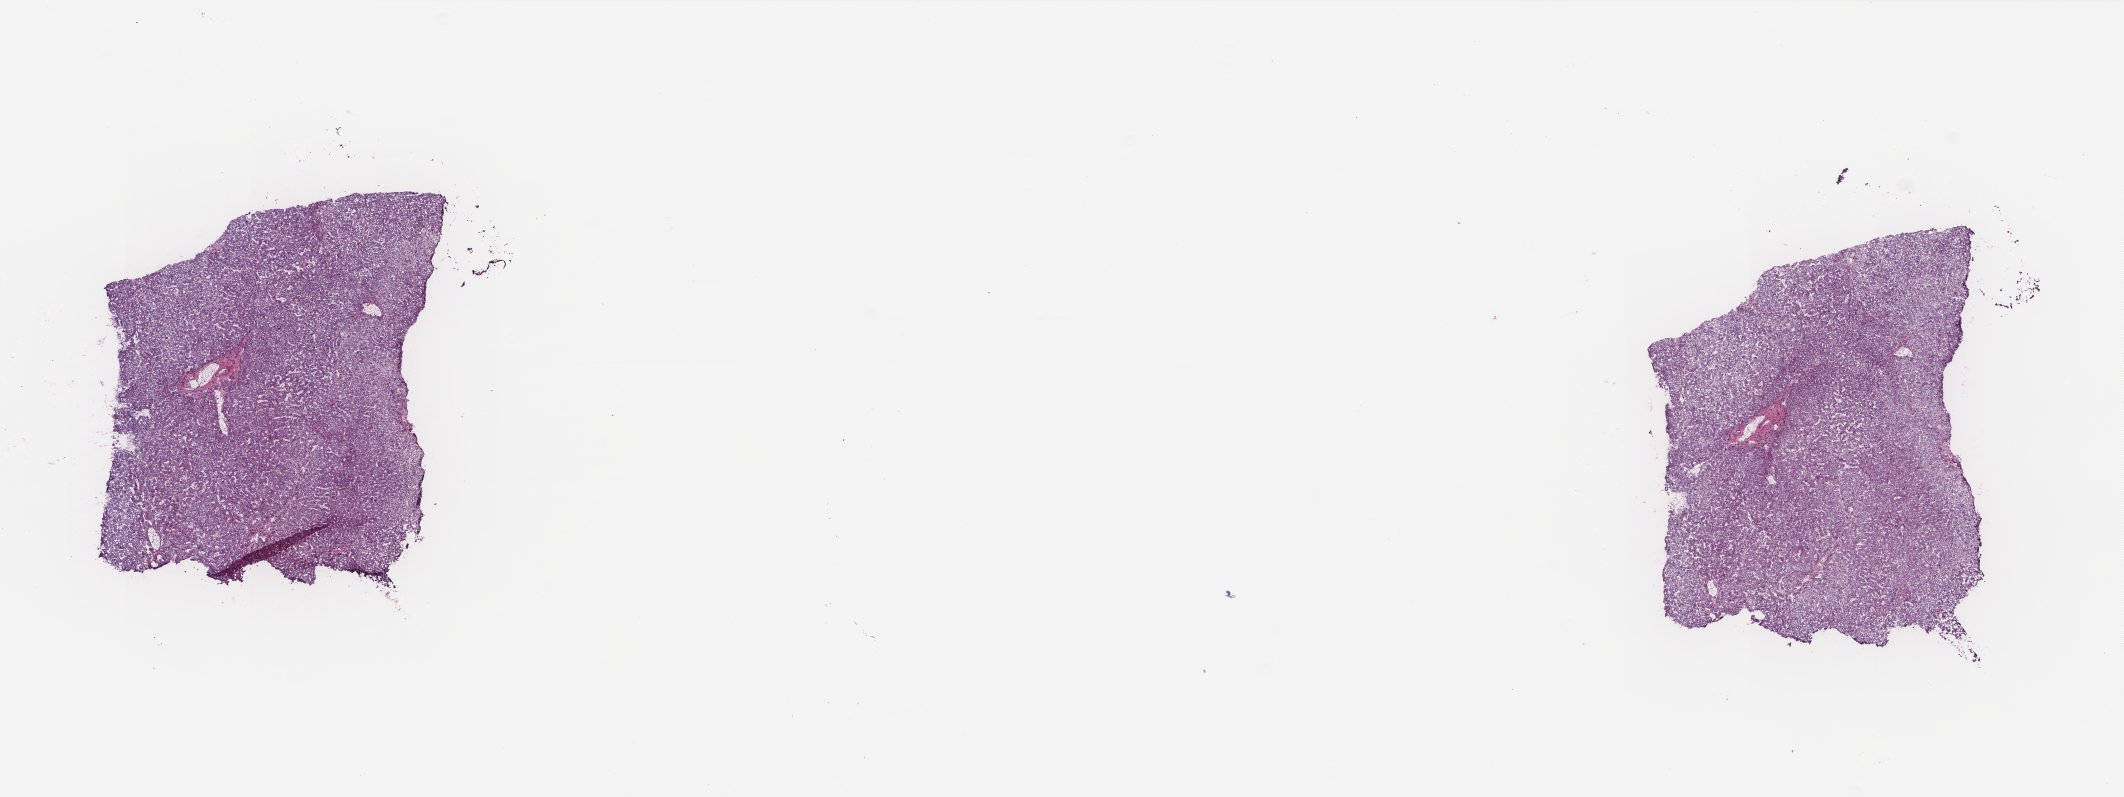
Digitized H&E-stained tissue section (whole slide) — shown as a low-resolution overview of the whole scanned area (about 17.0 x 6.4 mm); frozen section; solid tissue normal (non-tumour tissue) sample from the liver. Male patient; age at initial diagnosis 77 years. Composition of this section per pathologist review: tumour cells 0%, tumour nuclei 0%, normal cells 90%, stromal cells 10%, necrosis 0%. Inflammatory infiltration, as recorded: lymphocyte infiltration 1%, monocyte infiltration 1%, neutrophil infiltration 1%.
* this section: solid tissue normal sample (biorepository sample class)
* patient diagnosis: Hepatocellular carcinoma, NOS